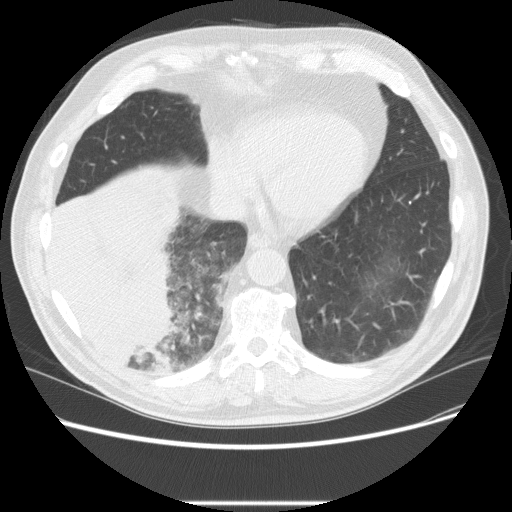
Low-dose screening chest CT, one axial slice; slice 65 of 233 in the series (ordered by position); reconstruction kernel STANDARD; lung window (W 1500 / L -600 HU); 2.5 mm slice thickness; 512 × 512 image matrix.
Outlined on this slice (expert manual segmentation):
- lesion 3 (tumor, lower lobe of right lung): bounding box (x1, y1, x2, y2) in pixels: (50, 196, 180, 366)